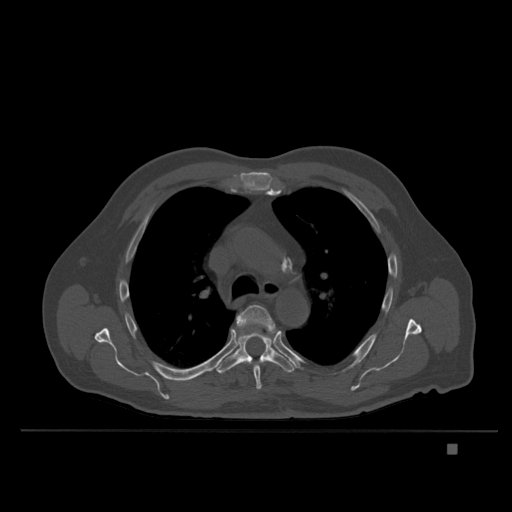
CT including the spine, one axial slice. Position 266 of 435 along the scan axis. Bone window (W 1800 / L 400 HU). 1.5 mm slice thickness. 512 × 512 image matrix. Male patient, age 73 years. From the clinical record (not read from this slice): primary cancer: skin.
Annotated regions visible in this slice (semi-automatic segmentation, software-assisted and operator-edited):
- T5 vertebra: bounding box <236,305,275,390> (left, top, right, bottom; pixels)
- T6 vertebra: <215,332,295,374>
- T7 vertebra: <235,340,237,347>